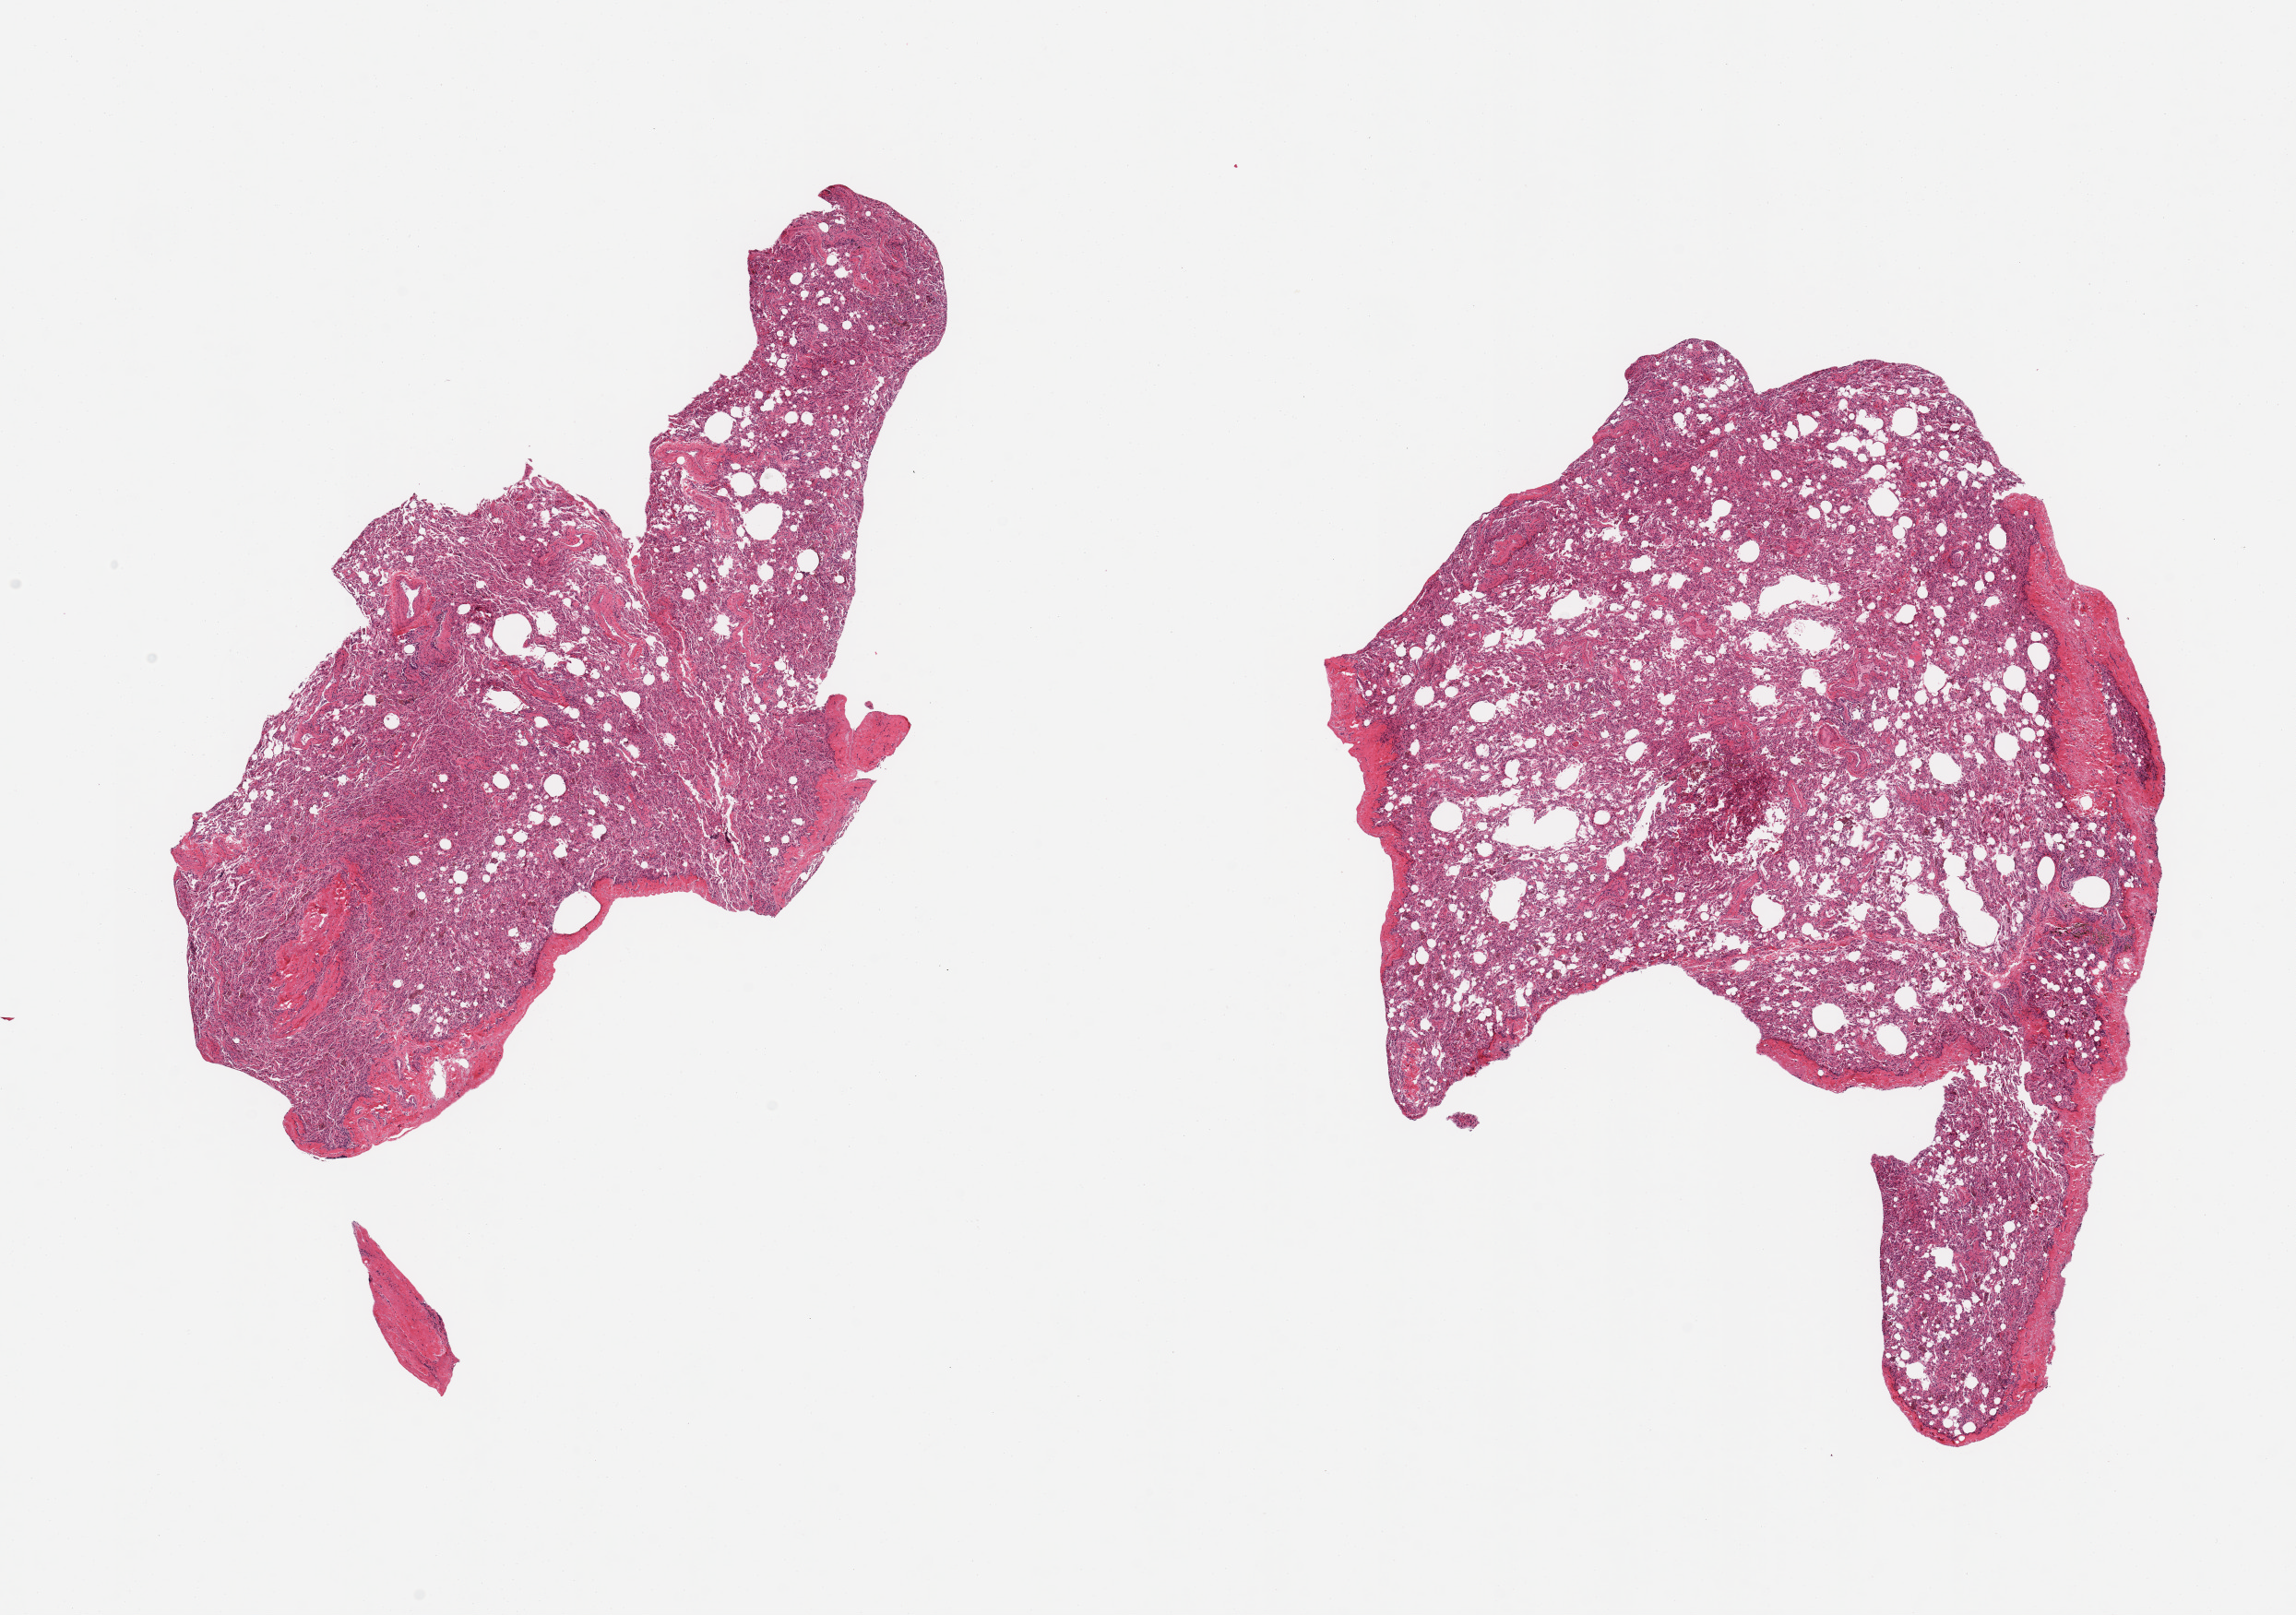
Whole-slide image, H&E stain — low-resolution overview of the scanned area, about 19.7 x 13.9 mm (from a 20x scan), PAXgene-fixed, paraffin-embedded tissue, sampled site (target tissue): lung, donor tissue sample. Donor sex: female.
• review note (as recorded): 2 pieces; include pleura (target is 1 cm below pleura), atelectasis, numerous pigmented macrophages